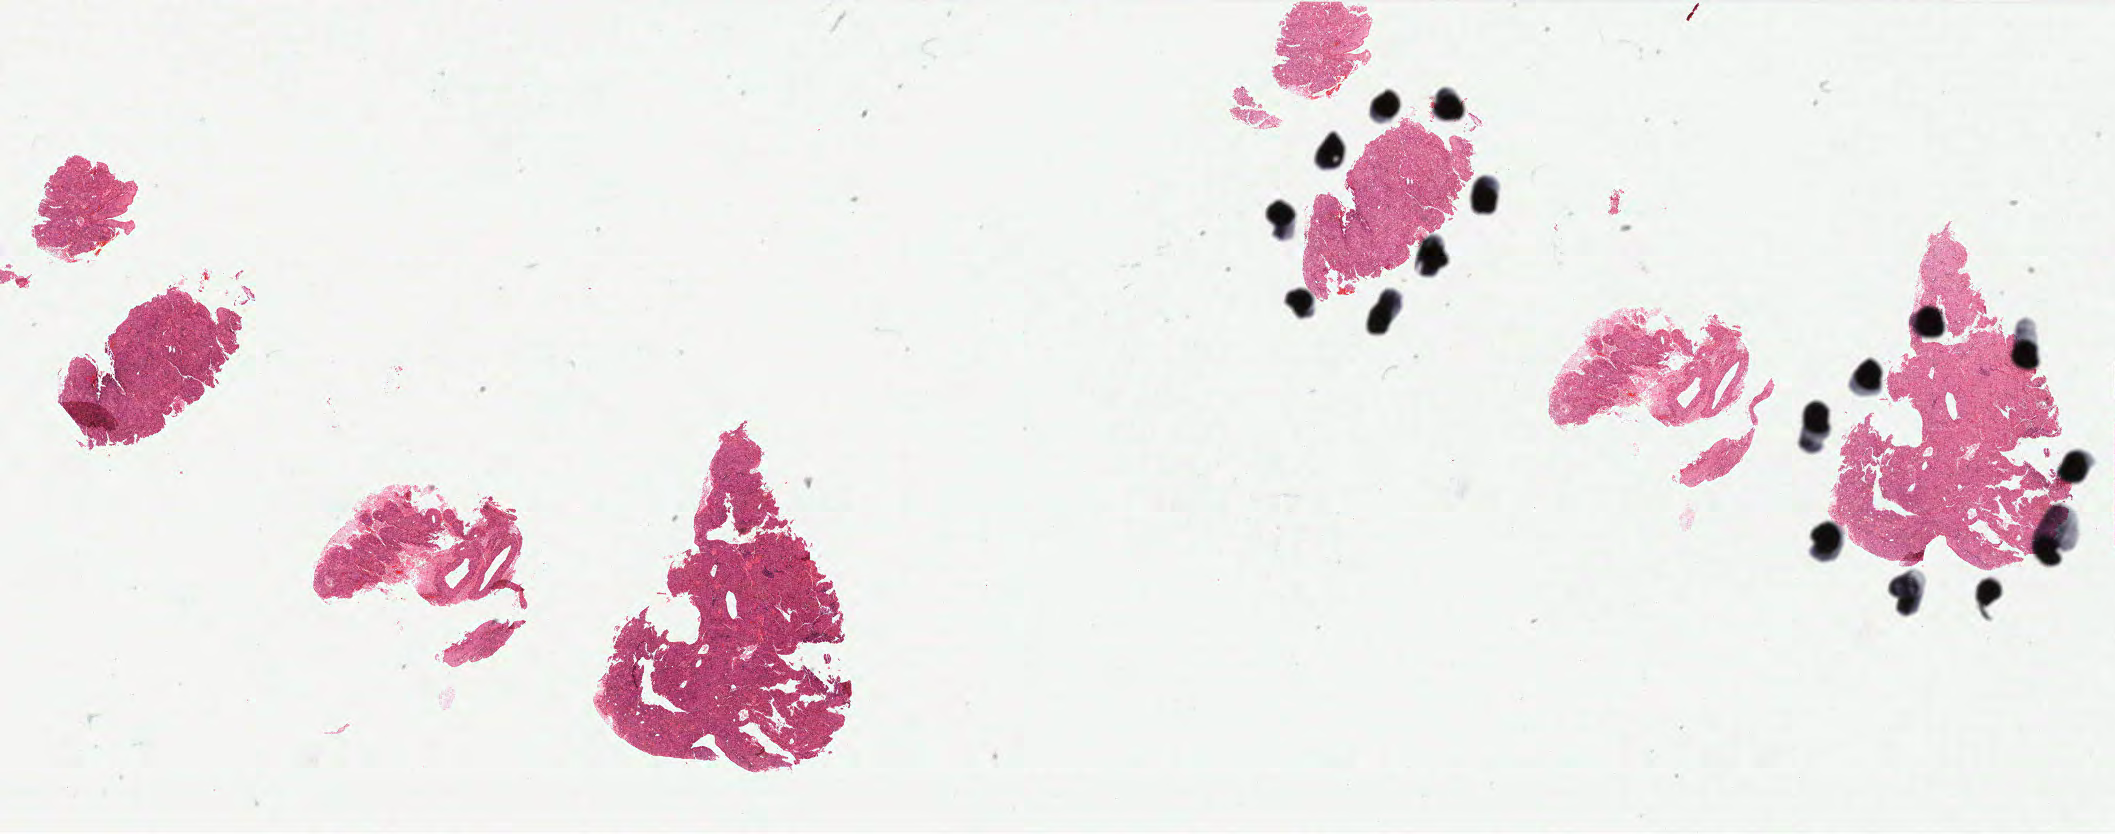
Whole-slide histology image, H&E, low-resolution overview of the scanned area, about 33.9 x 13.3 mm (from a 40x scan). Formalin-fixed paraffin-embedded (FFPE) diagnostic section. Cervix, primary tumour sample. Female patient; age at initial diagnosis 51 years. Histologic grade: G2 (moderately differentiated).
- diagnosis: Squamous cell carcinoma, NOS (cervix uteri)
- FIGO stage: IIB